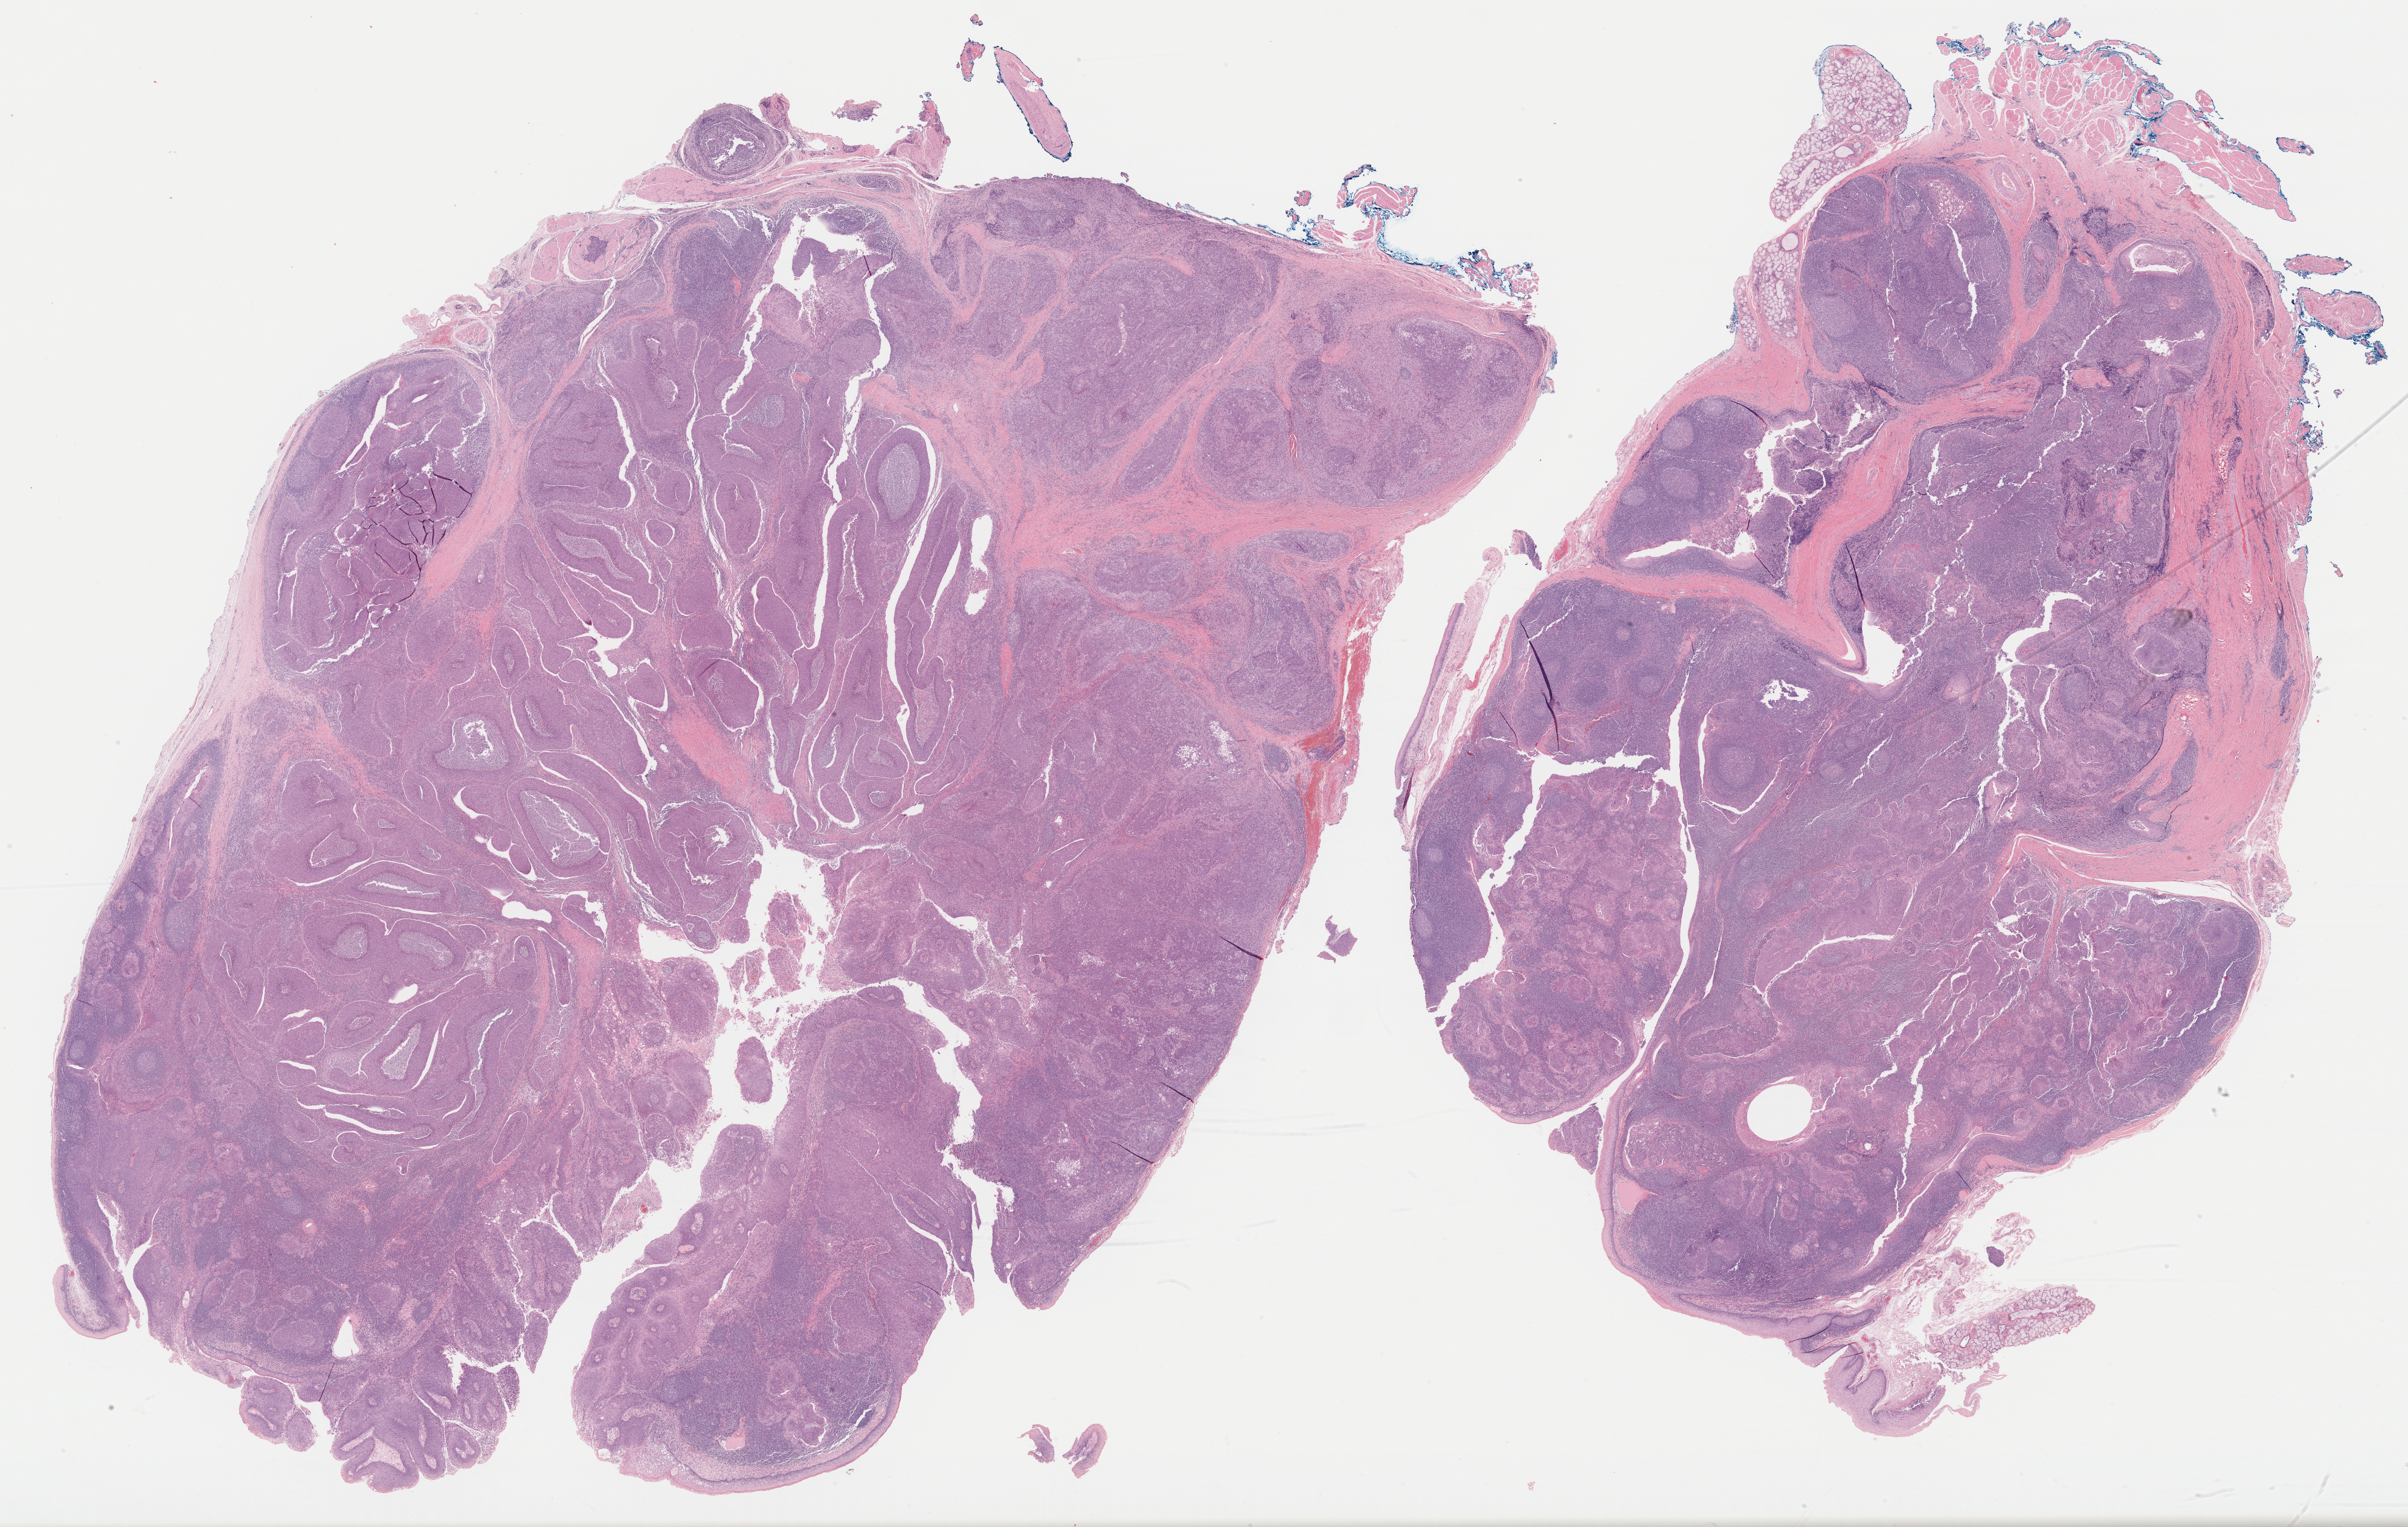
Digitized H&E tissue section (whole slide) — a low-resolution overview of the entire scanned area, about 31.4 x 19.9 mm (acquisition: 40x scan); formalin-fixed paraffin-embedded (FFPE) diagnostic section; sample: primary tumour, head and neck. Male patient; age at initial diagnosis 54 years. Histologic grade: G3 (poorly differentiated).
AJCC pathologic stage: IVA (6th edition). Laterality: right. Histologic diagnosis: Basaloid squamous cell carcinoma (tonsil, NOS).